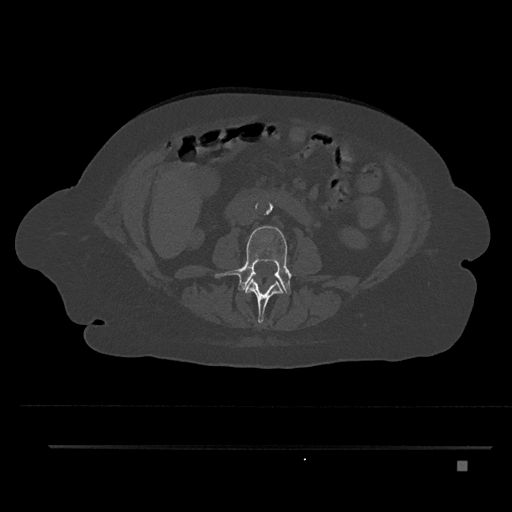
CT including the spine, one axial slice; slice 144 of 797 in the series (ordered by position); 120 kVp; bone window (W 1800 / L 400 HU); 0.5 mm slice thickness; 512 × 512 image matrix, field of view 437 × 437 mm. Female patient, age 76 years. Case-level facts recorded for this patient, not image findings: primary cancer: lung; vertebrae with lytic lesions (as recorded): T11, L3.
Outlined on this slice (semi-automatically segmented with operator editing):
- L2 vertebra: bounding box <245,278,284,324> (left, top, right, bottom; pixels)
- L3 vertebra: <215,226,291,295>